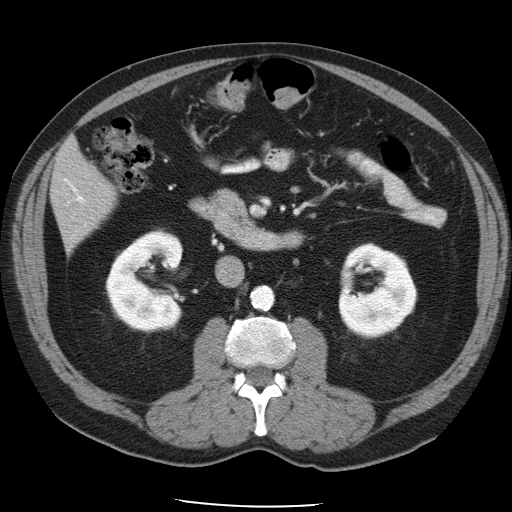
Contrast-enhanced abdominal CT, one axial slice; intravenous contrast given; soft-tissue window (W 400 / L 40 HU); 5 mm slice thickness; 512 × 512 image matrix, field of view 395 × 395 mm. Male patient, age 68 years. From the clinical record (not read from this slice): diagnosis: colorectal cancer liver metastases, imaged before liver resection; multiple liver metastases: yes; largest metastasis: 1.7 cm.
Structures marked on this image (manually delineated by an expert):
- liver: box from (x=52, y=139) to (x=115, y=246) px
- planned liver remnant (the part of the liver to remain after resection): (x=61, y=139)–(x=115, y=198)
- portal vein (with intrahepatic branches): (x=65, y=179)–(x=87, y=226)